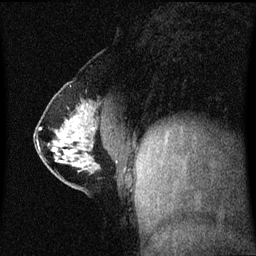
Breast MRI (dynamic contrast-enhanced), one sagittal slice; slice 23 of 60 in the series (ordered by position); dynamic contrast-enhanced series, image 2 of 3 at this slice position (ordered by acquisition); 1.5 T; TE 4.2 ms, TR 8.4 ms; 2 mm slice thickness; 256 × 256 image matrix, field of view 210 × 210 mm. Female patient, age 40 years. Case-level facts recorded for this patient, not image findings: setting: breast cancer imaged before/during neoadjuvant chemotherapy; receptor status: triple-negative.
Outlined on this slice (semi-automatic segmentation, software-assisted and operator-edited):
- analysis volume of interest (the breast-tissue region the enhancement analysis was run in; not a lesion): bounding box [x1, y1, x2, y2] px = [35, 112, 116, 188]
- tumour enhancement mask (voxels above the 70 % enhancement threshold inside the analysis volume of interest): [61, 136, 65, 138]